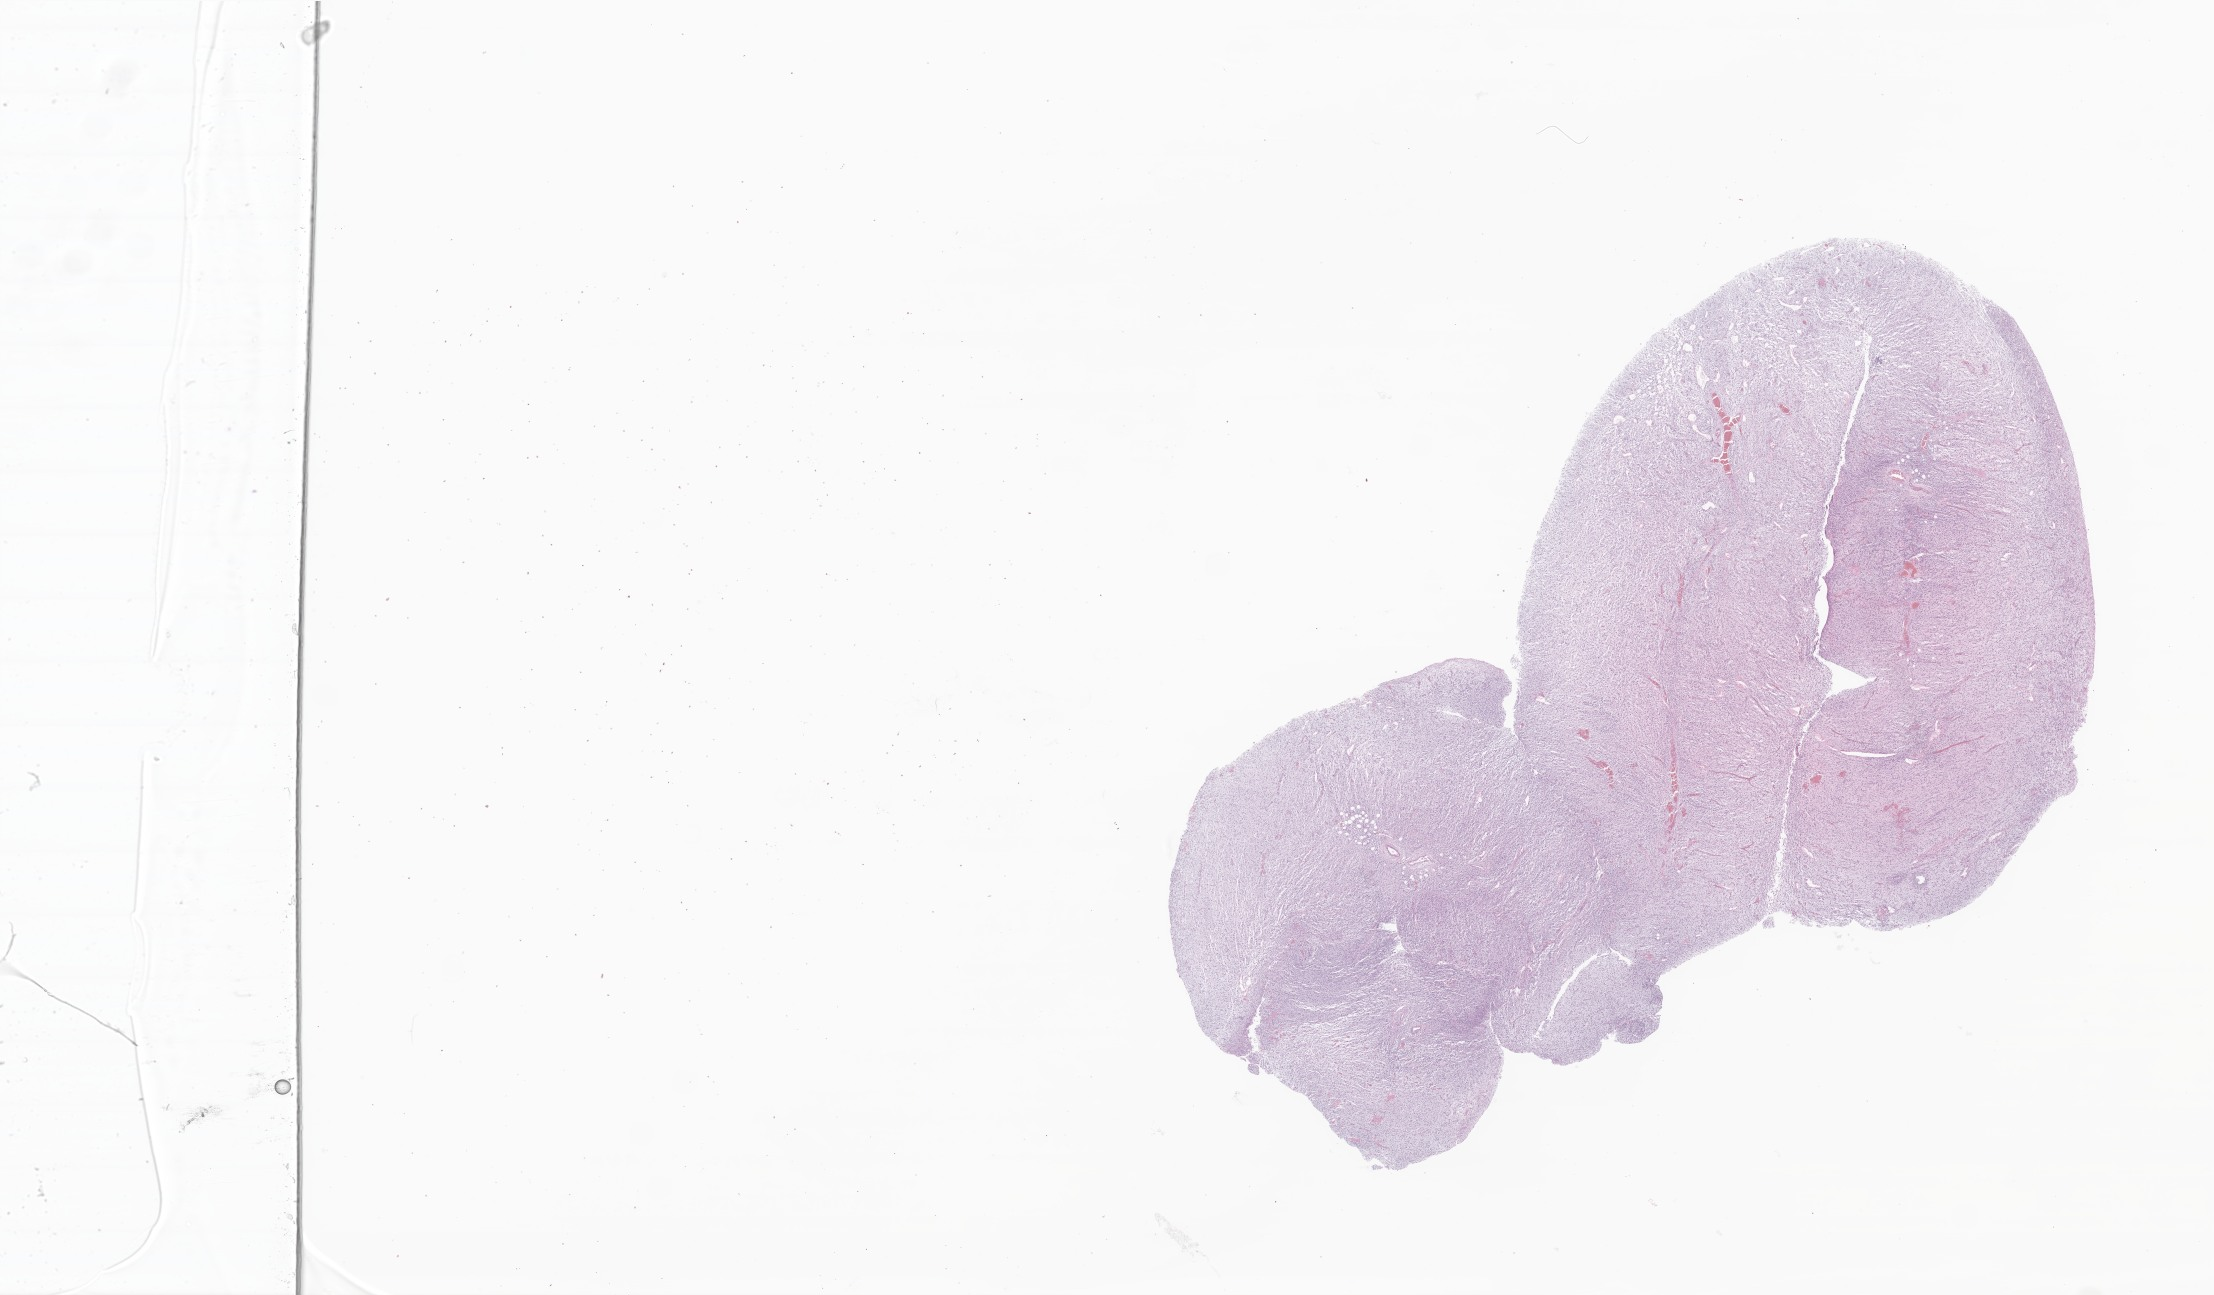
Whole-slide image, H&E stain of tumor tissue from the abdomen — shown as a low-resolution overview of the whole scanned area (about 37.3 x 21.8 mm), formalin-fixed, paraffin-embedded (FFPE) tissue. Patient: female, age 64 months (5 years 4 months).
Diagnosis: Rhabdomyosarcoma, NOS.